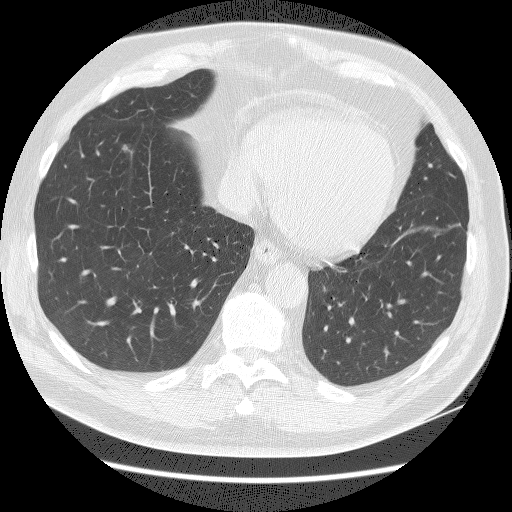
Axial slice from a low-dose chest CT screening exam, baseline annual screen, lung window (W 1500 / L -600 HU), 2.5 mm slice thickness, slice 114 of 161 in the series. Male, age 65 years at enrolment. Current smoker at enrolment.
Expert reader's lesion annotation, box from (x=106, y=132) to (x=152, y=169) px. The screening reader recorded 3 non-calcified nodules or masses ≥4 mm on this exam (right lower lobe, right middle lobe, left upper lobe); which of them this box marks is not recorded. Official screen result: positive, change unspecified: nodule(s) >= 4 mm or enlarging nodule(s), mass(es), or other non-specific abnormalities suspicious for lung cancer. Lung cancer was diagnosed 132 days after this screen: adenocarcinoma, NOS, right lower lobe, poorly differentiated (G3), stage IA (AJCC 6th edition), 10 mm at pathology.